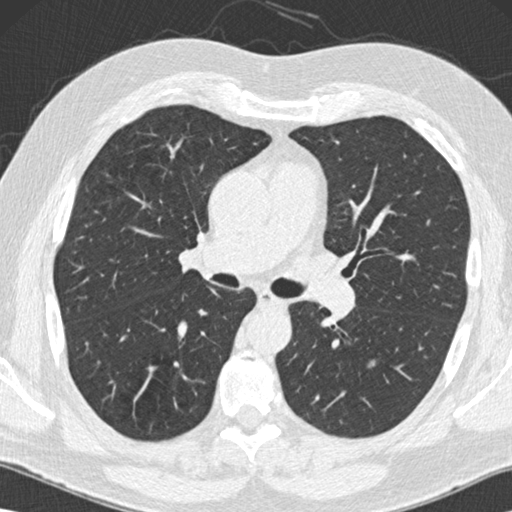
Low-dose screening chest CT, one axial slice; position 85 of 152 along the scan axis; reconstruction kernel B30f; lung window (W 1500 / L -600 HU); 2 mm slice thickness; 512 × 512 image matrix, field of view 350 × 350 mm.
Annotated regions visible in this slice (expert manual segmentation):
- lesion 2 (nodule, lower lobe of left lung): bounding box [x1, y1, x2, y2] px = [369, 361, 375, 367]